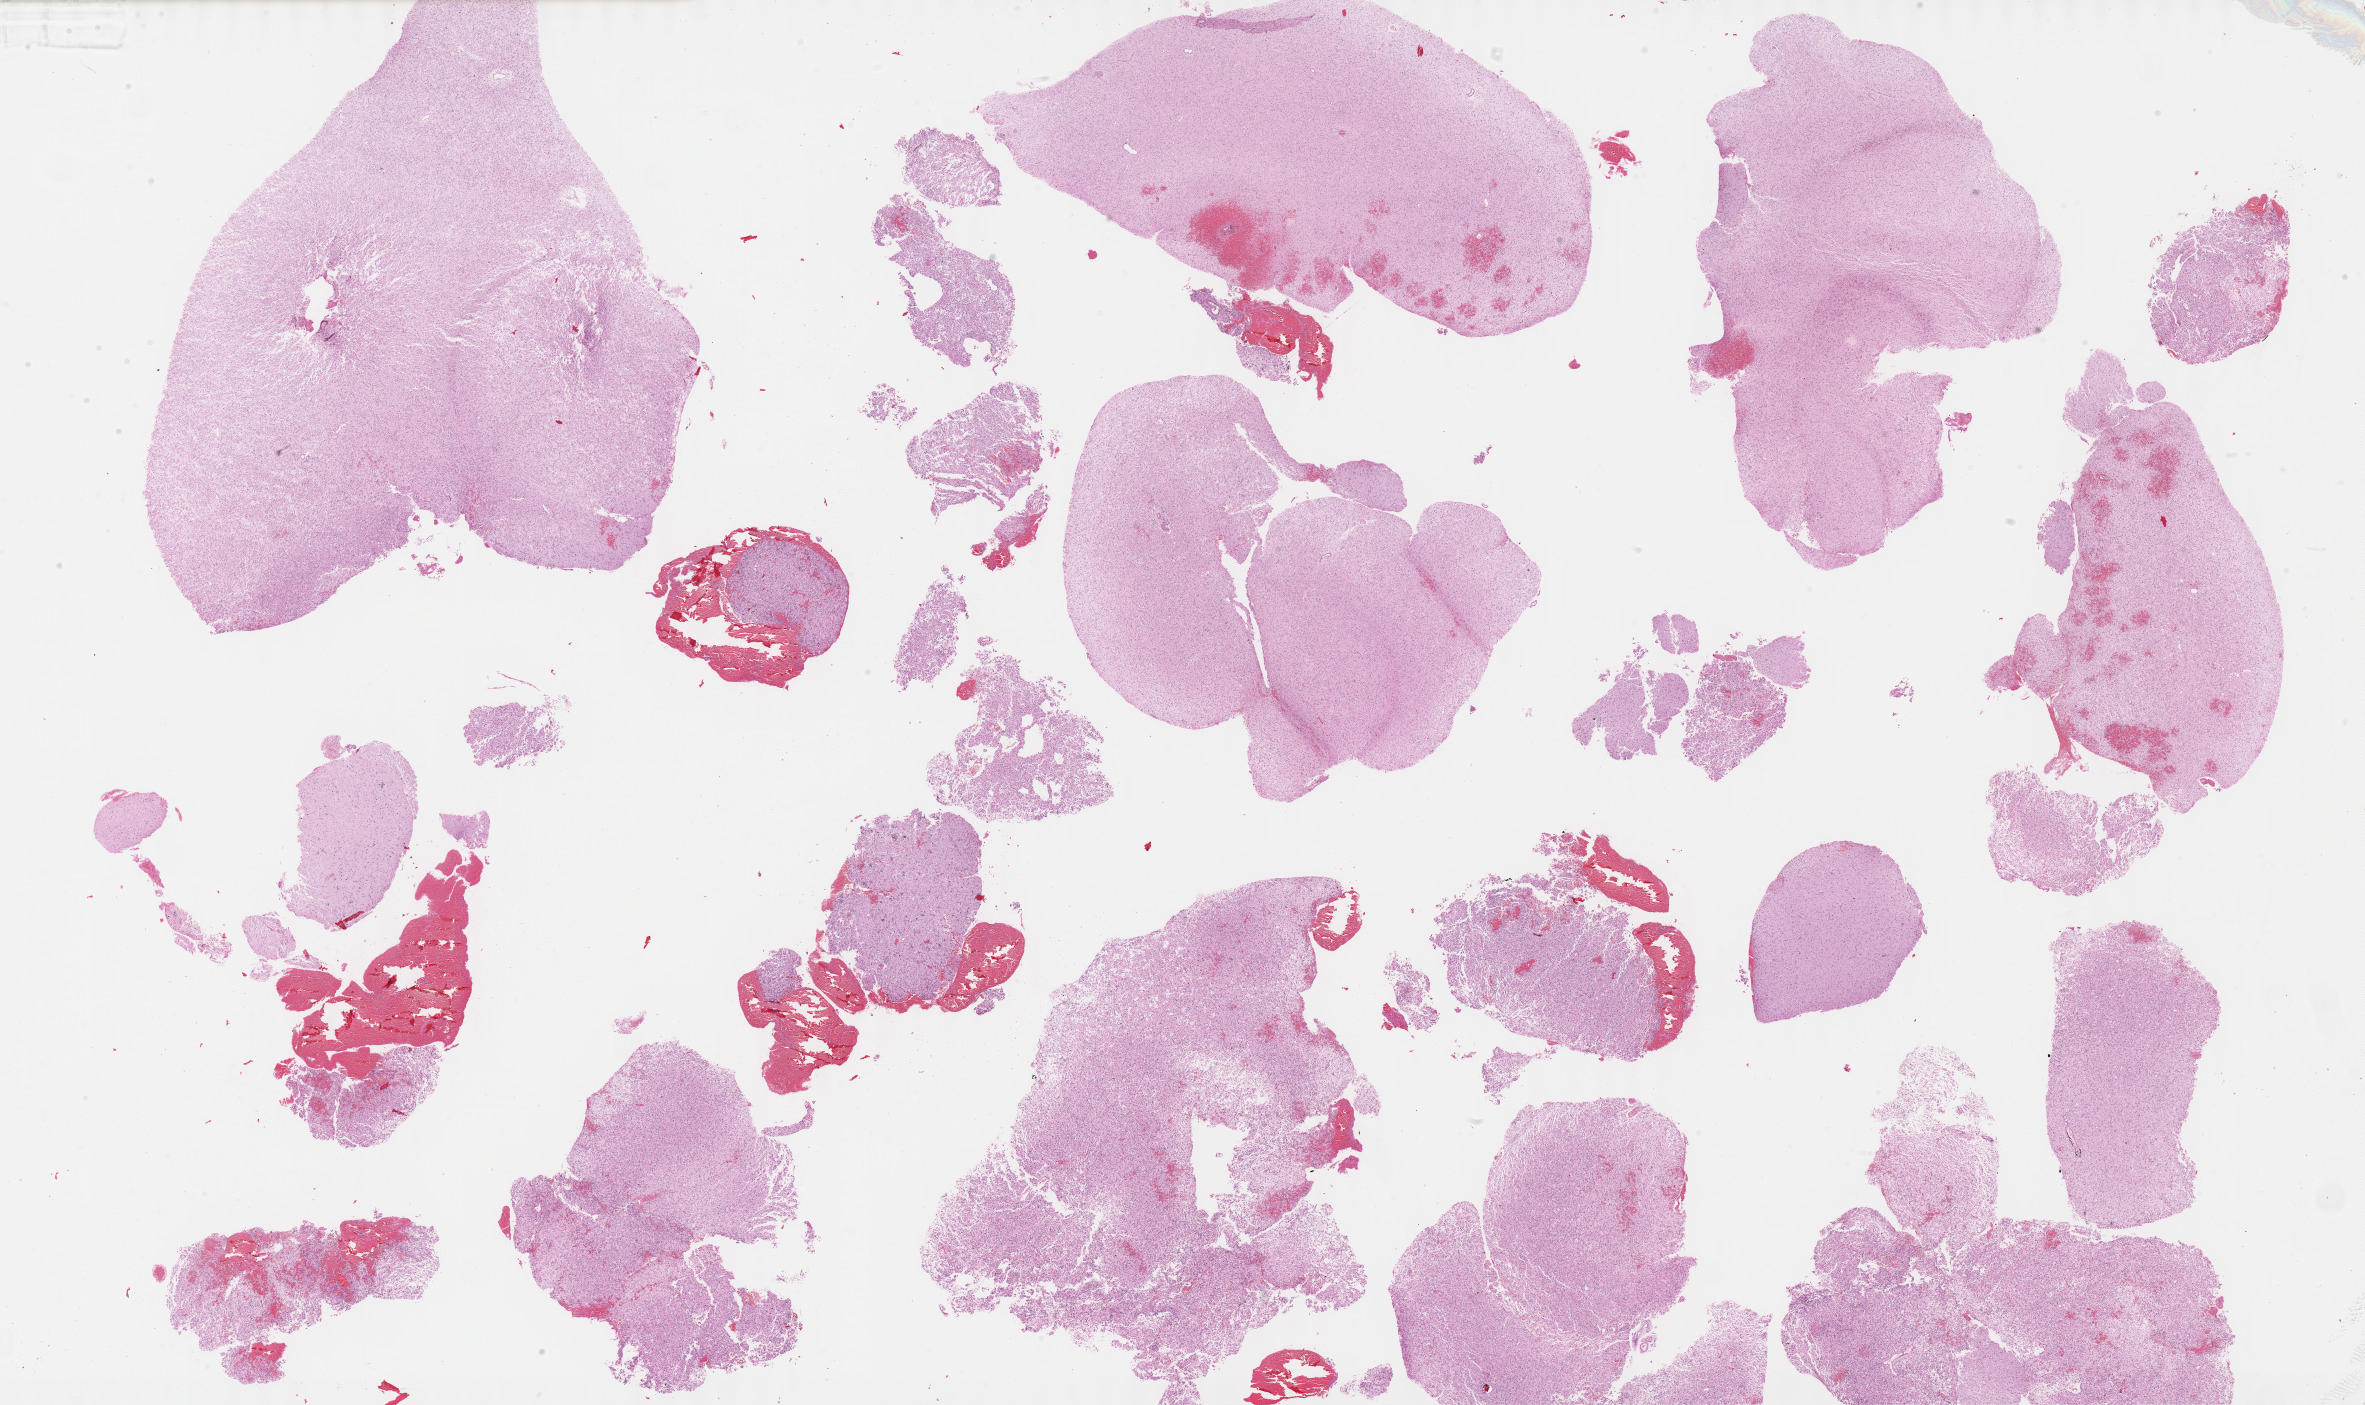
Digitized H&E-stained tissue section (whole slide), a low-resolution overview of the entire scanned area, about 38.2 x 22.7 mm, formalin-fixed paraffin-embedded (FFPE) diagnostic section, sample: recurrent tumour, brain. Female patient; age at initial diagnosis 42 years.
This section: recurrent tumour. Patient diagnosis: Oligodendroglioma, NOS.